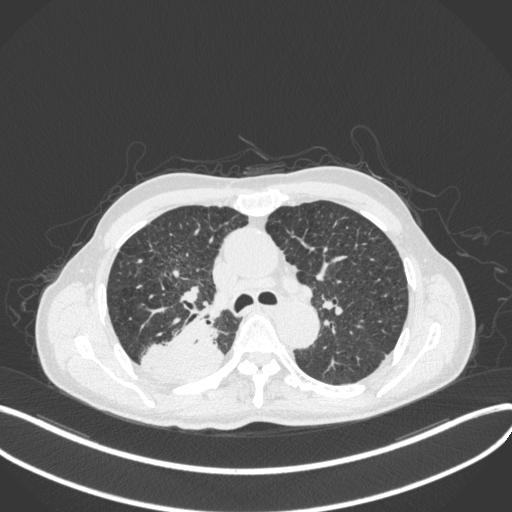
Chest CT, one axial slice; position 301 of 423 along the scan axis; reconstruction kernel B31f; 120 kVp; lung window (W 1500 / L -600 HU); 1 mm slice thickness; 512 × 512 image matrix. Patient: male, 79 years. Case-level facts recorded for this patient, not image findings: clinical TNM (as recorded): T3 N0 M0.
Annotated regions visible in this slice (rectangle marked by the reading radiologist):
- lung tumour (recorded histology: adenocarcinoma): bounding box [x1, y1, x2, y2] px = [136, 319, 227, 384]